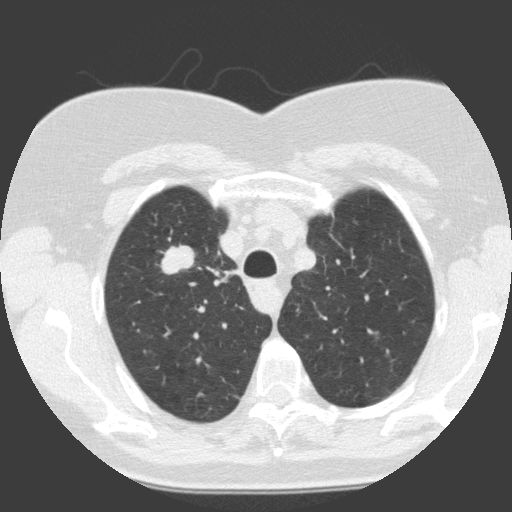
Chest CT (low-dose screening protocol), one axial image. Baseline annual screen. Lung window (W 1500 / L -600 HU). 2 mm slice thickness. Female participant, aged 68 years at enrolment. Current smoker at enrolment.
Lesion marked by an expert reader, bounding box [x1, y1, x2, y2] px = [154, 241, 201, 285]. Reader record for this screening exam (exam-level; its link to the box is not recorded): non-calcified nodule or mass ≥4 mm, right upper lobe, 19 × 12 mm, smooth margins, soft tissue attenuation. Later outcome: lung cancer diagnosed 30 days after this screen — squamous cell carcinoma, NOS, right upper lobe, moderately differentiated (G2), stage IA (AJCC 6th edition), 28 mm at pathology.